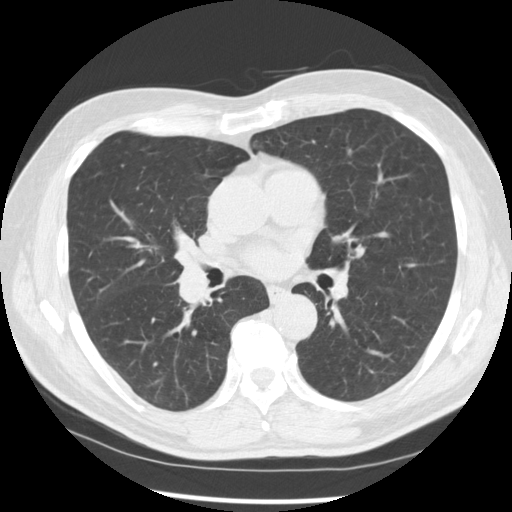
Low-dose screening chest CT, one axial slice. 120 kVp. Lung window (W 1500 / L -600 HU). 512 × 512 image matrix.
Annotated regions visible in this slice (manually delineated by an expert):
- lesion 1 (tumor, middle lobe of right lung): bounding box (x1, y1, x2, y2) in pixels: (178, 266, 210, 303)